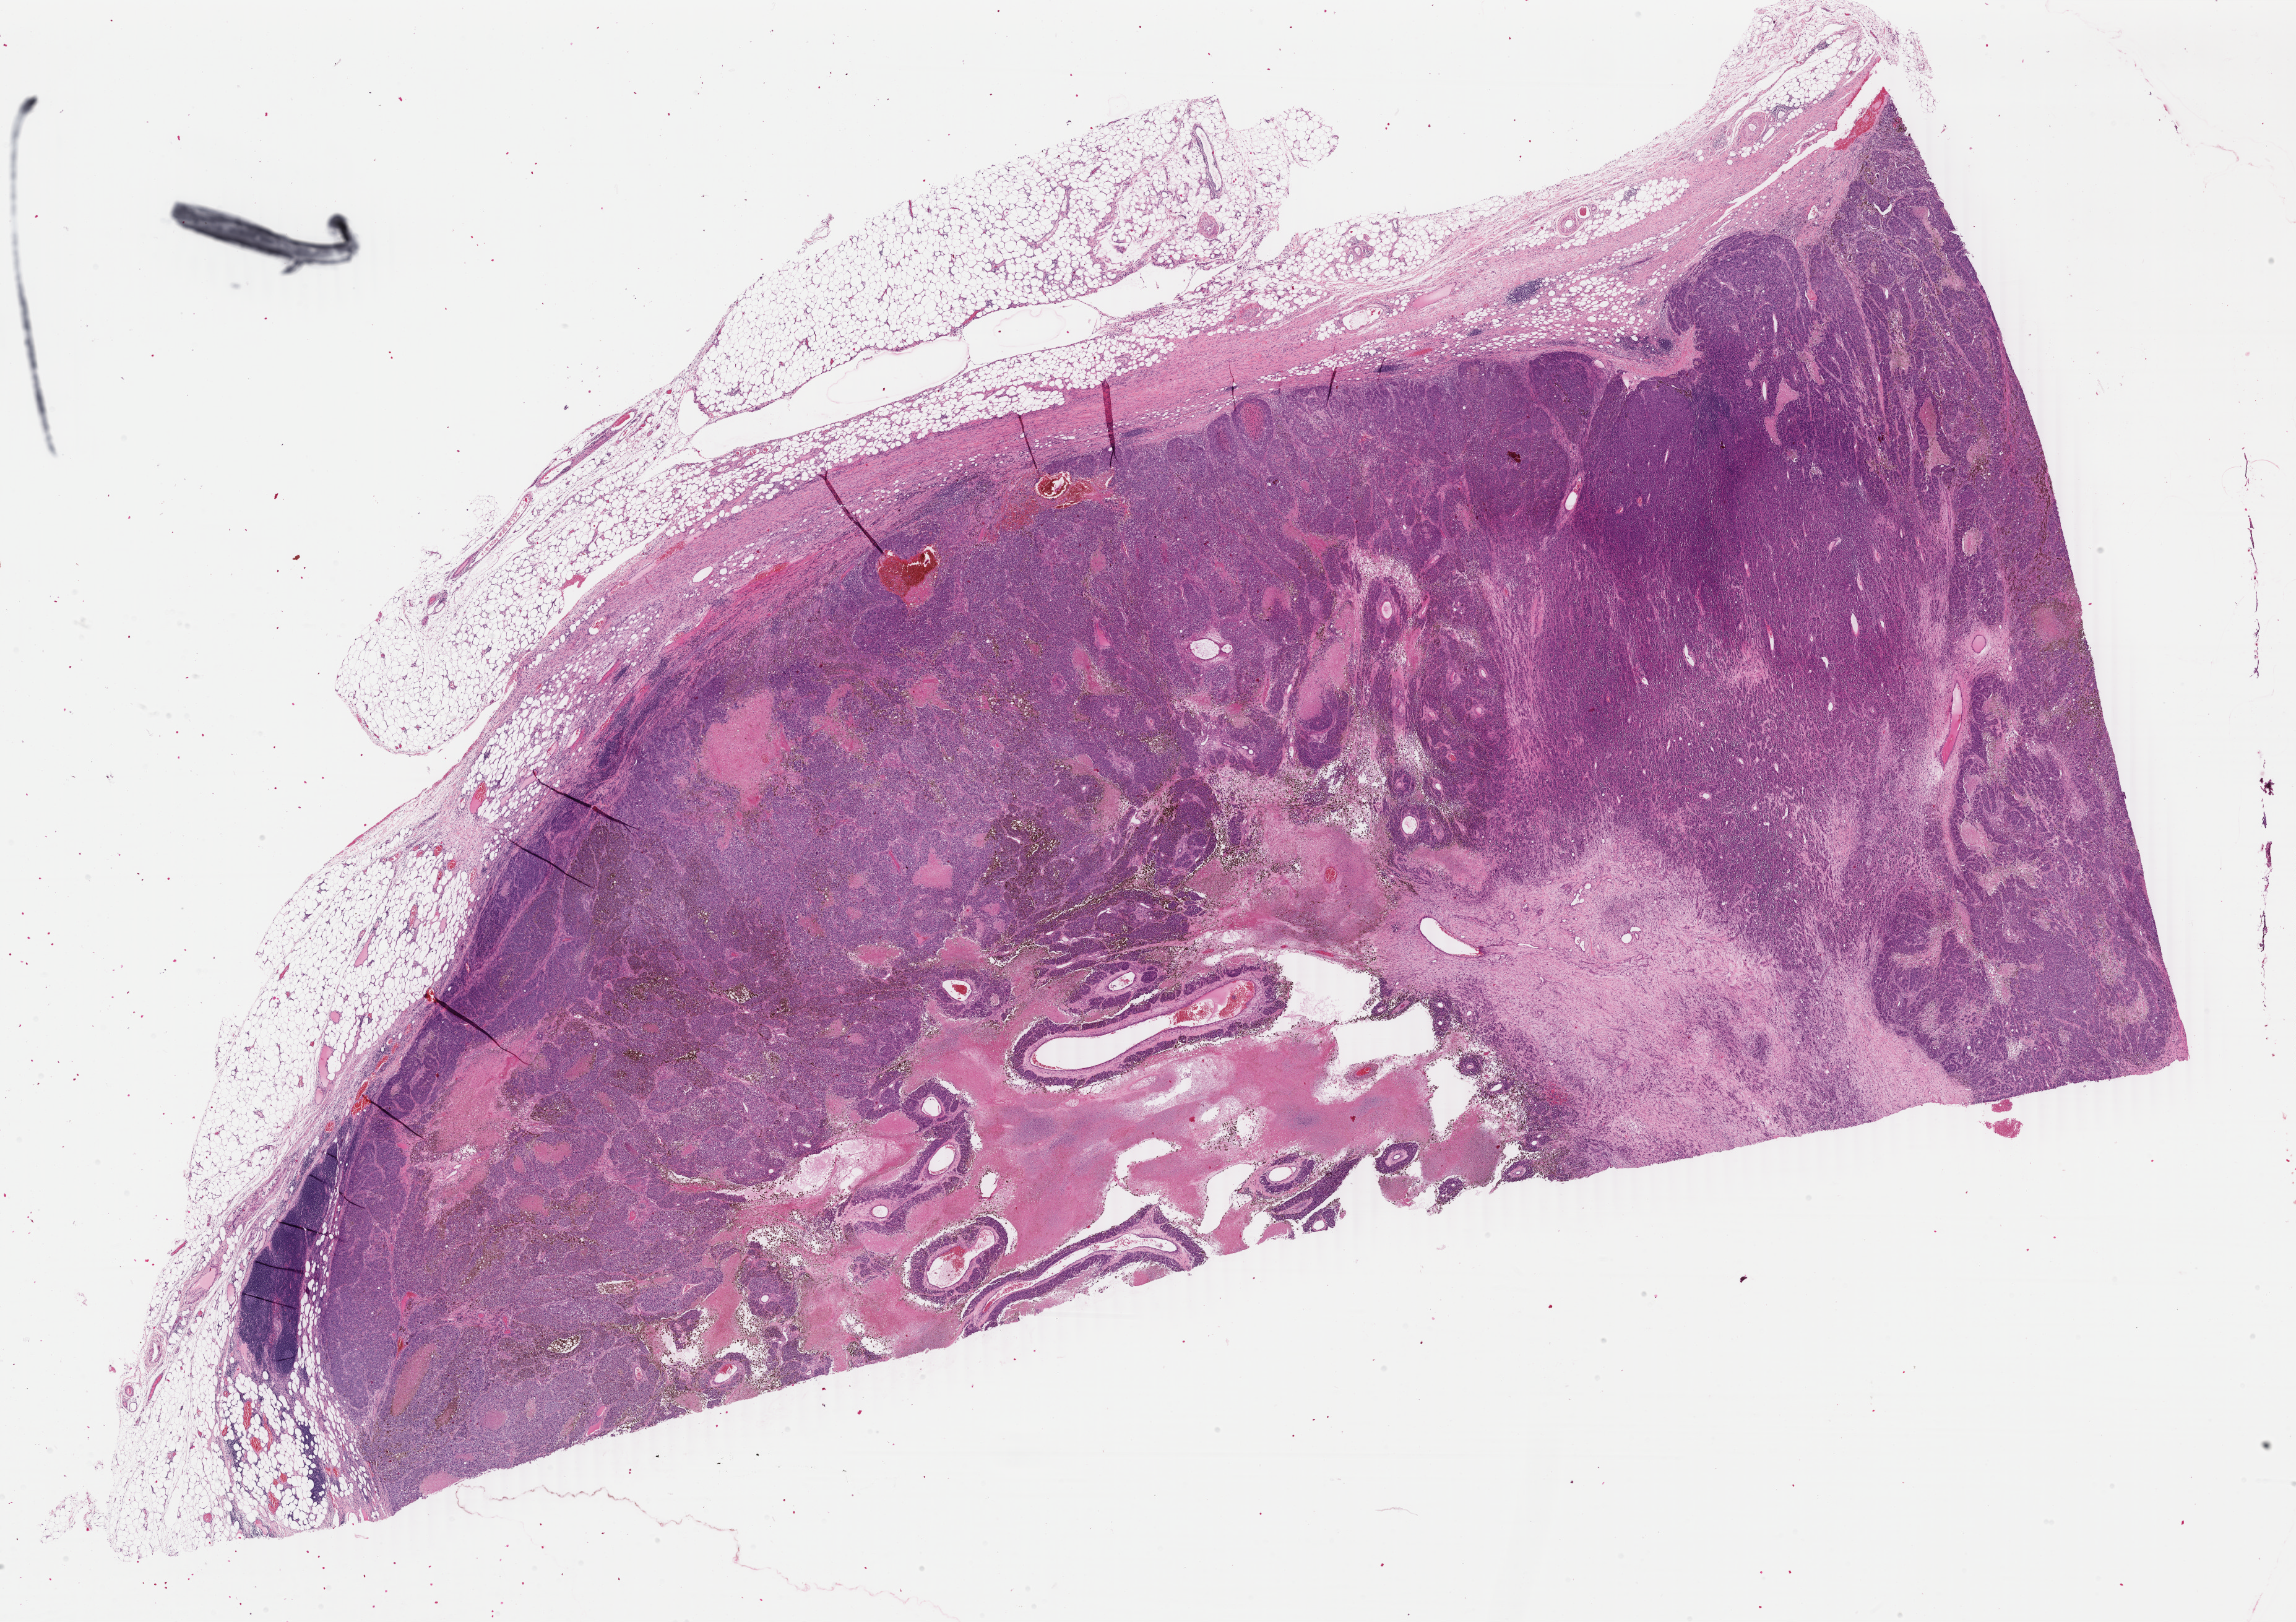
H&E whole-slide image, a low-resolution overview of the entire scanned area, about 29.5 x 20.8 mm (acquisition: 40x scan); FFPE section; primary tumour sample from the skin. Female patient; age at initial diagnosis 59 years.
- diagnosis: Malignant melanoma, NOS